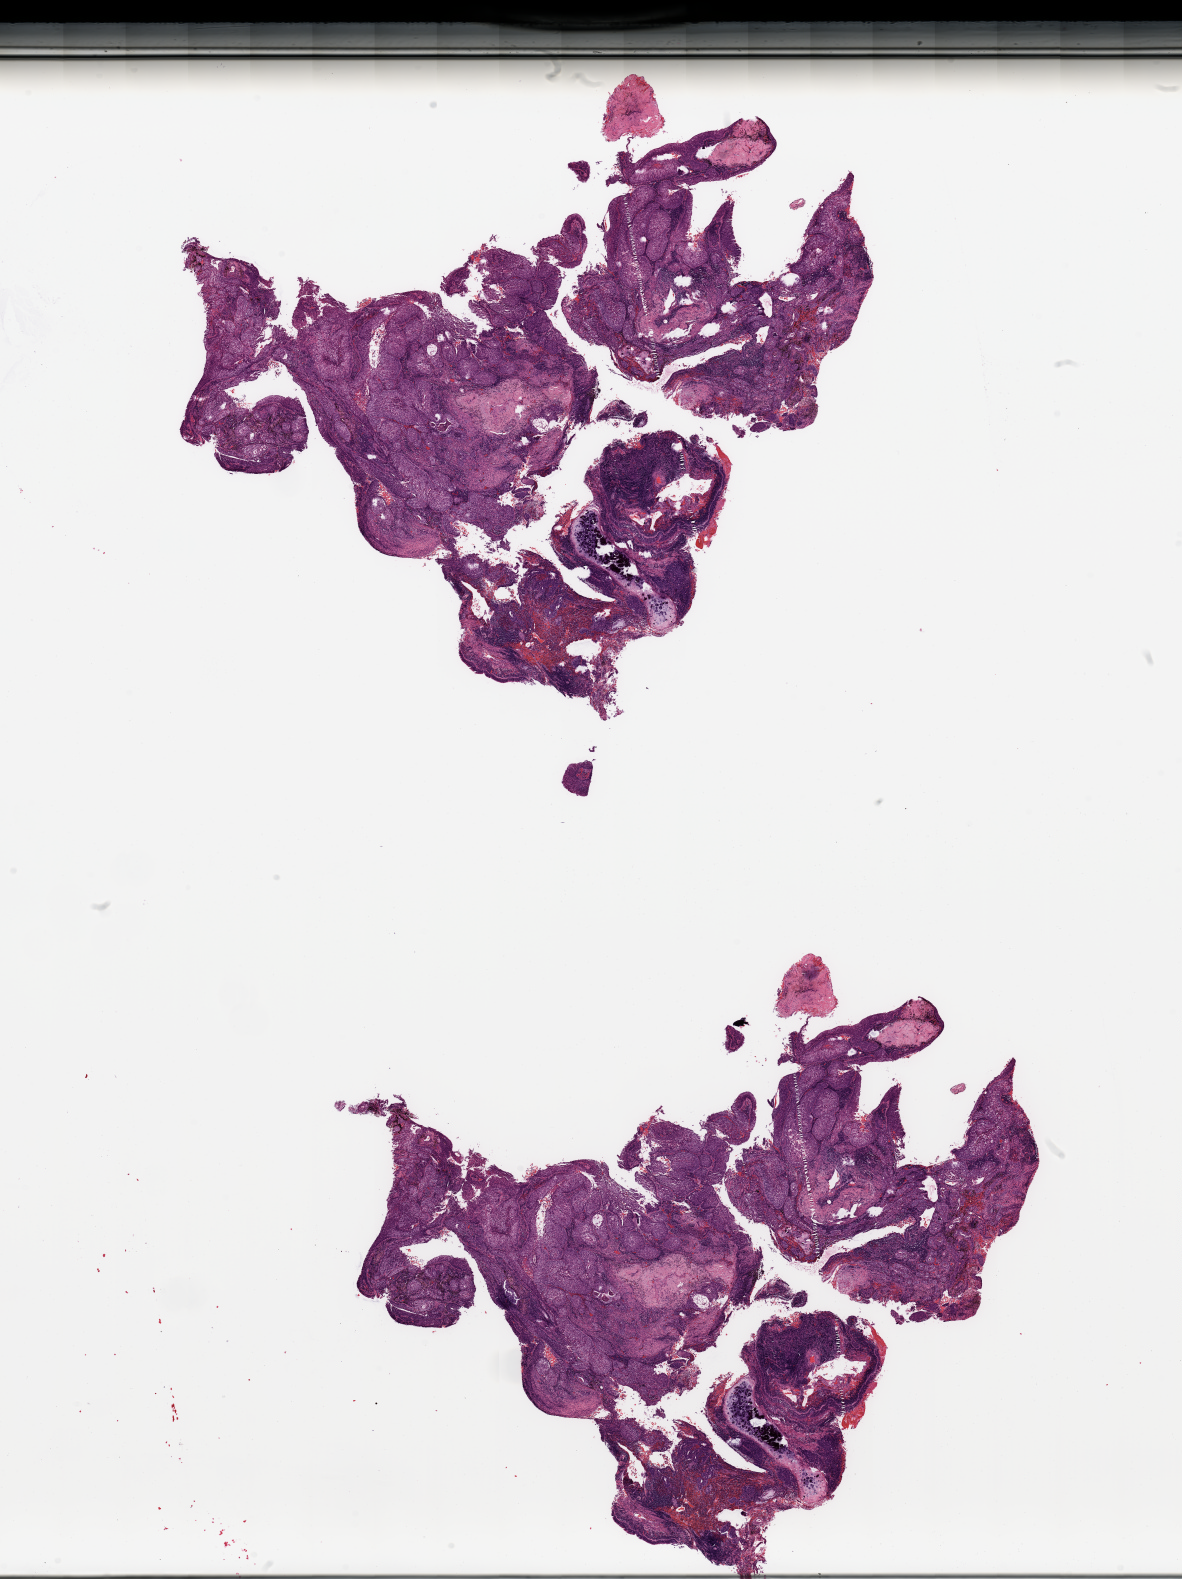
Whole-slide histology image, Hematoxylin and eosin (H&E) stained — a low-resolution overview of the entire scanned area, about 18.7 x 25.0 mm (slide scanned at 20x); tumour tissue sample, sampled site: lung. 71-year-old male patient. Histologic grade: G3 (poorly differentiated). Pathologist review of this section (percent, as recorded): tumour nuclei 90%, necrosis 5%.
* AJCC pathologic stage: IIB
* diagnosis: Squamous cell carcinoma, NOS
* primary tumour site (as recorded): right lower lobe